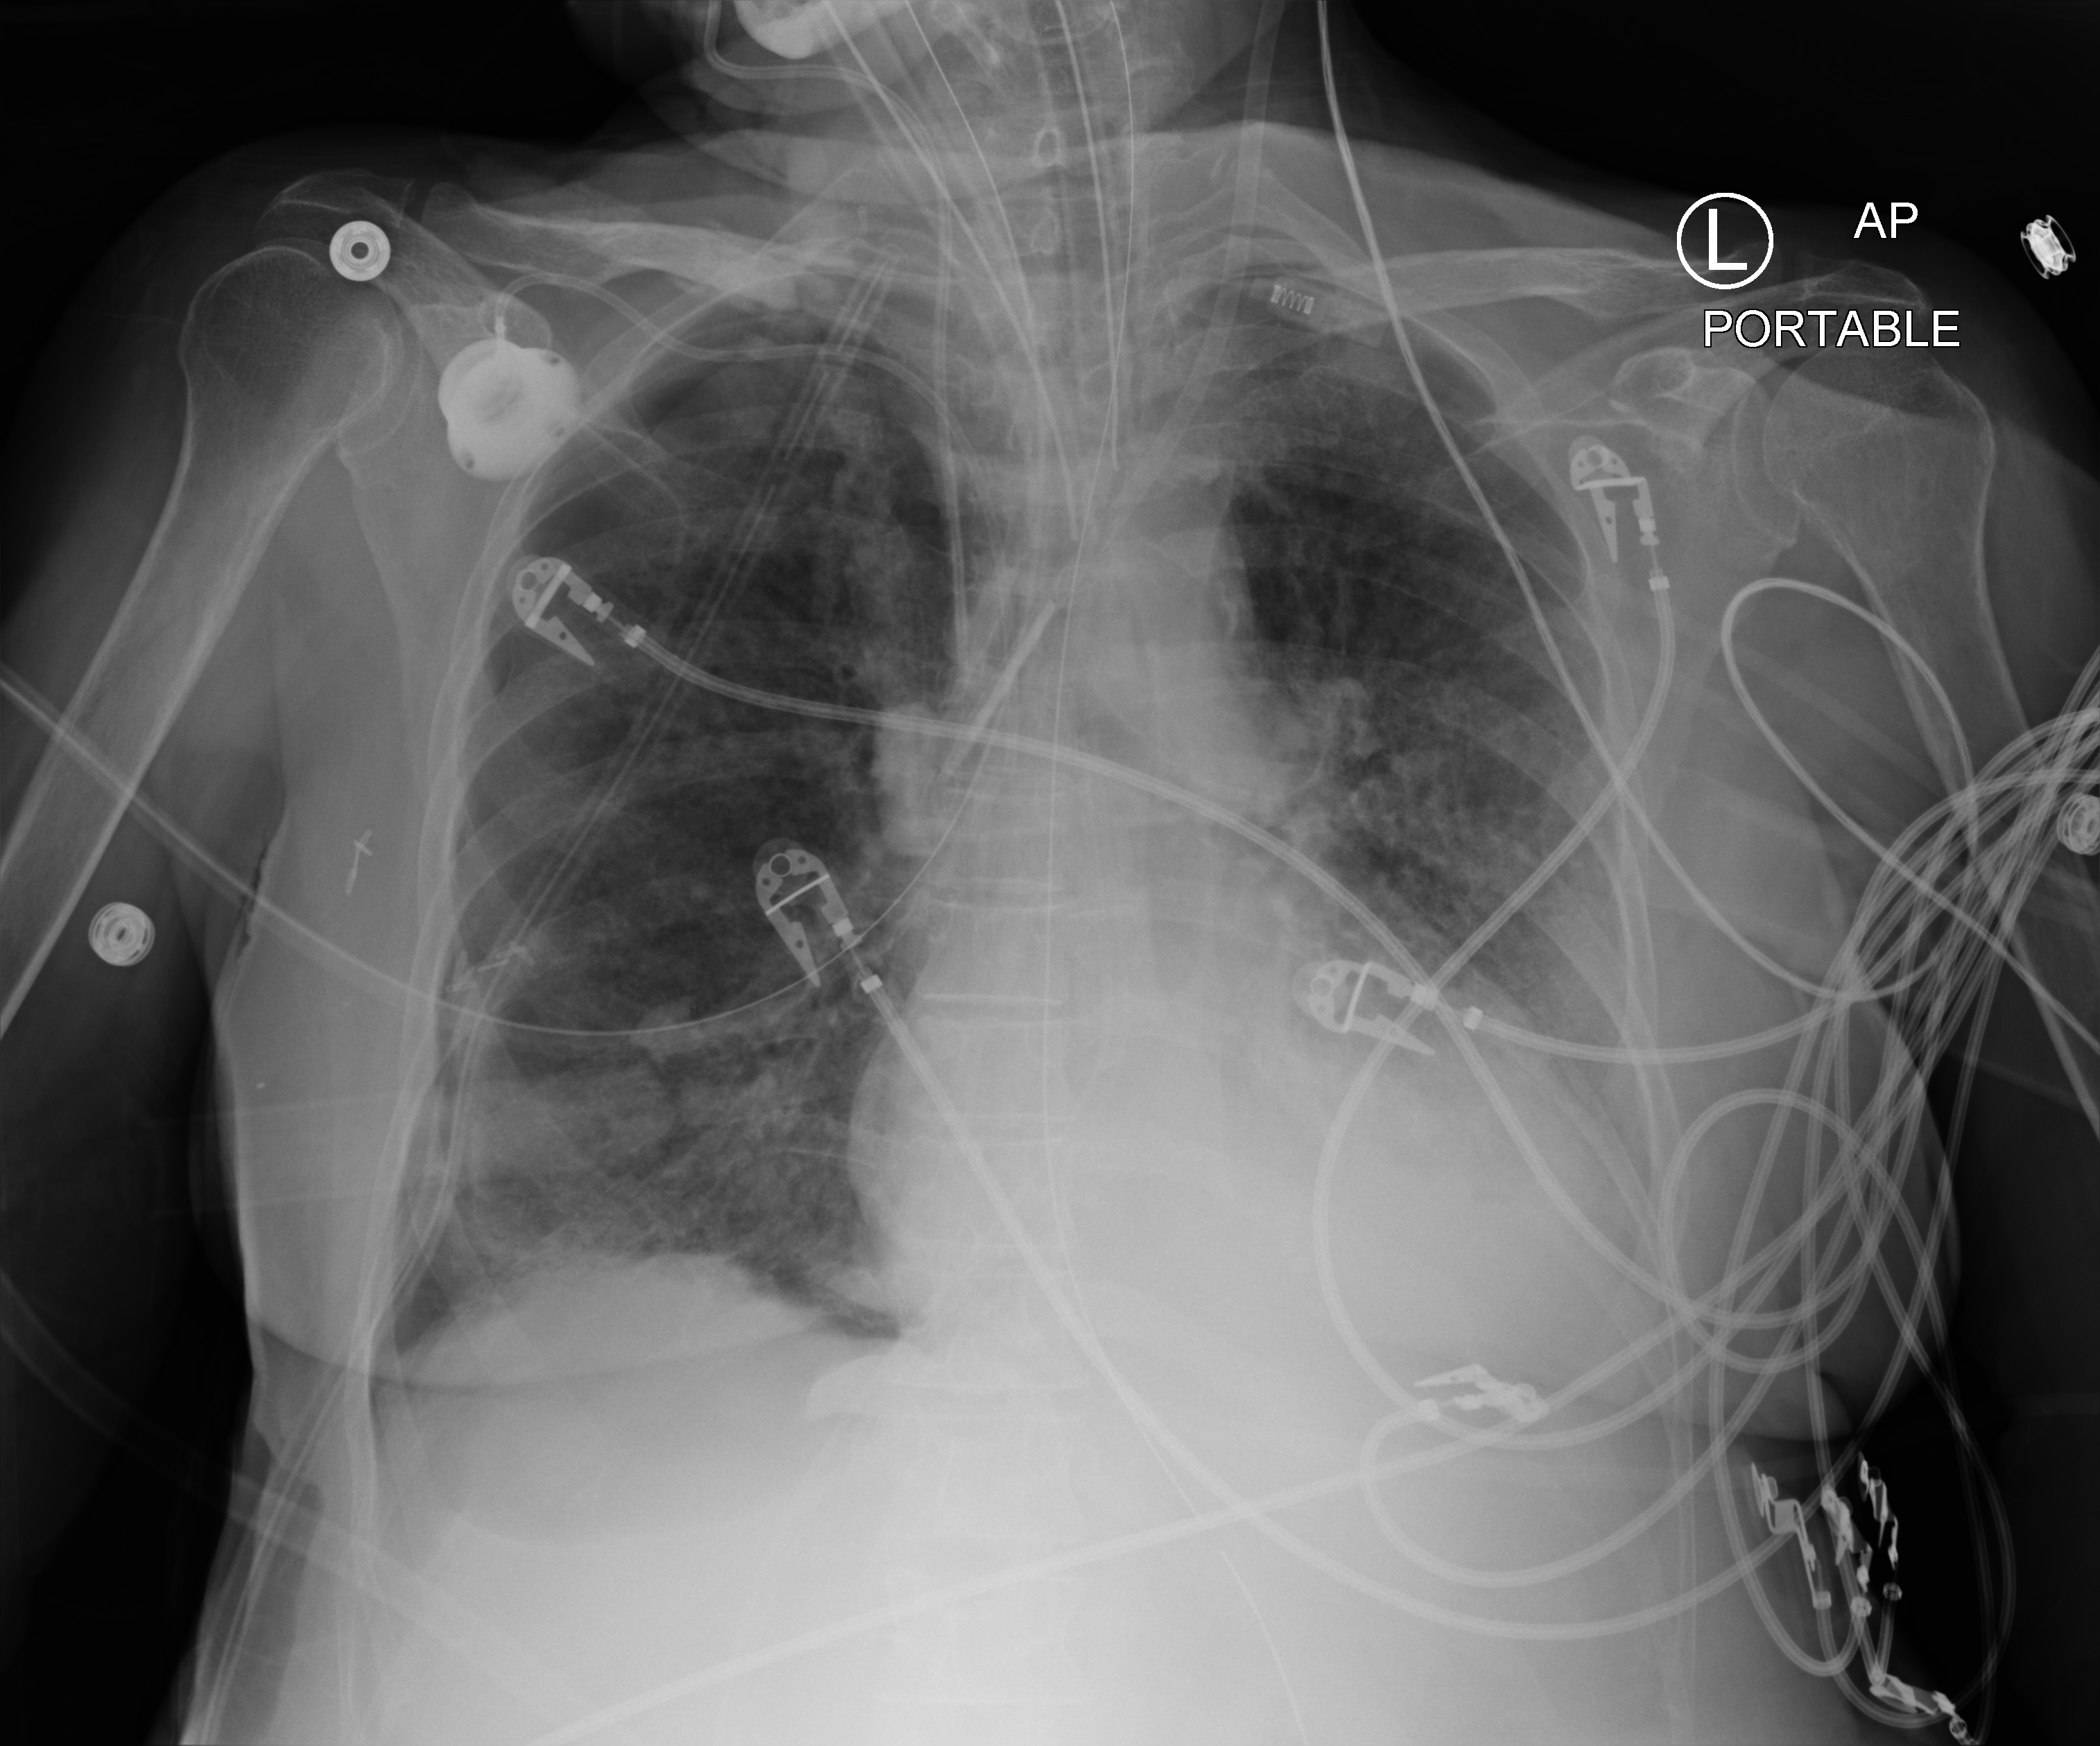
Chest X-ray (portable). Patient hospitalised with COVID-19; female, aged 60–74 years.
Hospital-stay facts (about this admission, not read from this image; timing relative to this image not recorded): length of hospital stay: 43 days.